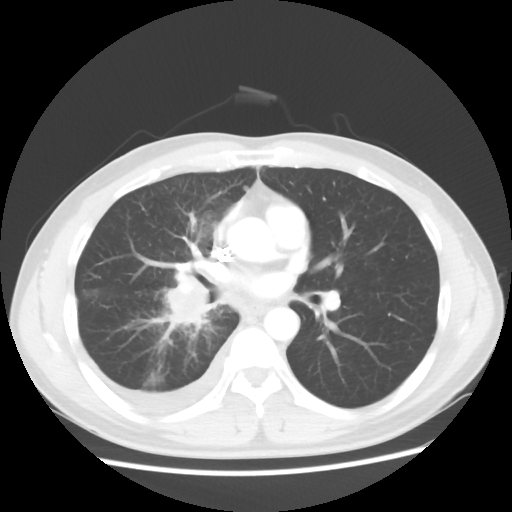
Chest CT, one axial slice. Reconstruction kernel STANDARD. 120 kVp. Lung window (W 1500 / L -600 HU). 5 mm slice thickness. 512 × 512 image matrix, field of view 360 × 360 mm. Male patient, age 46 years. From the clinical record (not read from this slice): clinical TNM (as recorded): T2 N3 M1.
Outlined on this slice (bounding box drawn by a radiologist):
- lung tumour (recorded histology: adenocarcinoma): bounding box [x1, y1, x2, y2] px = [151, 263, 224, 340]